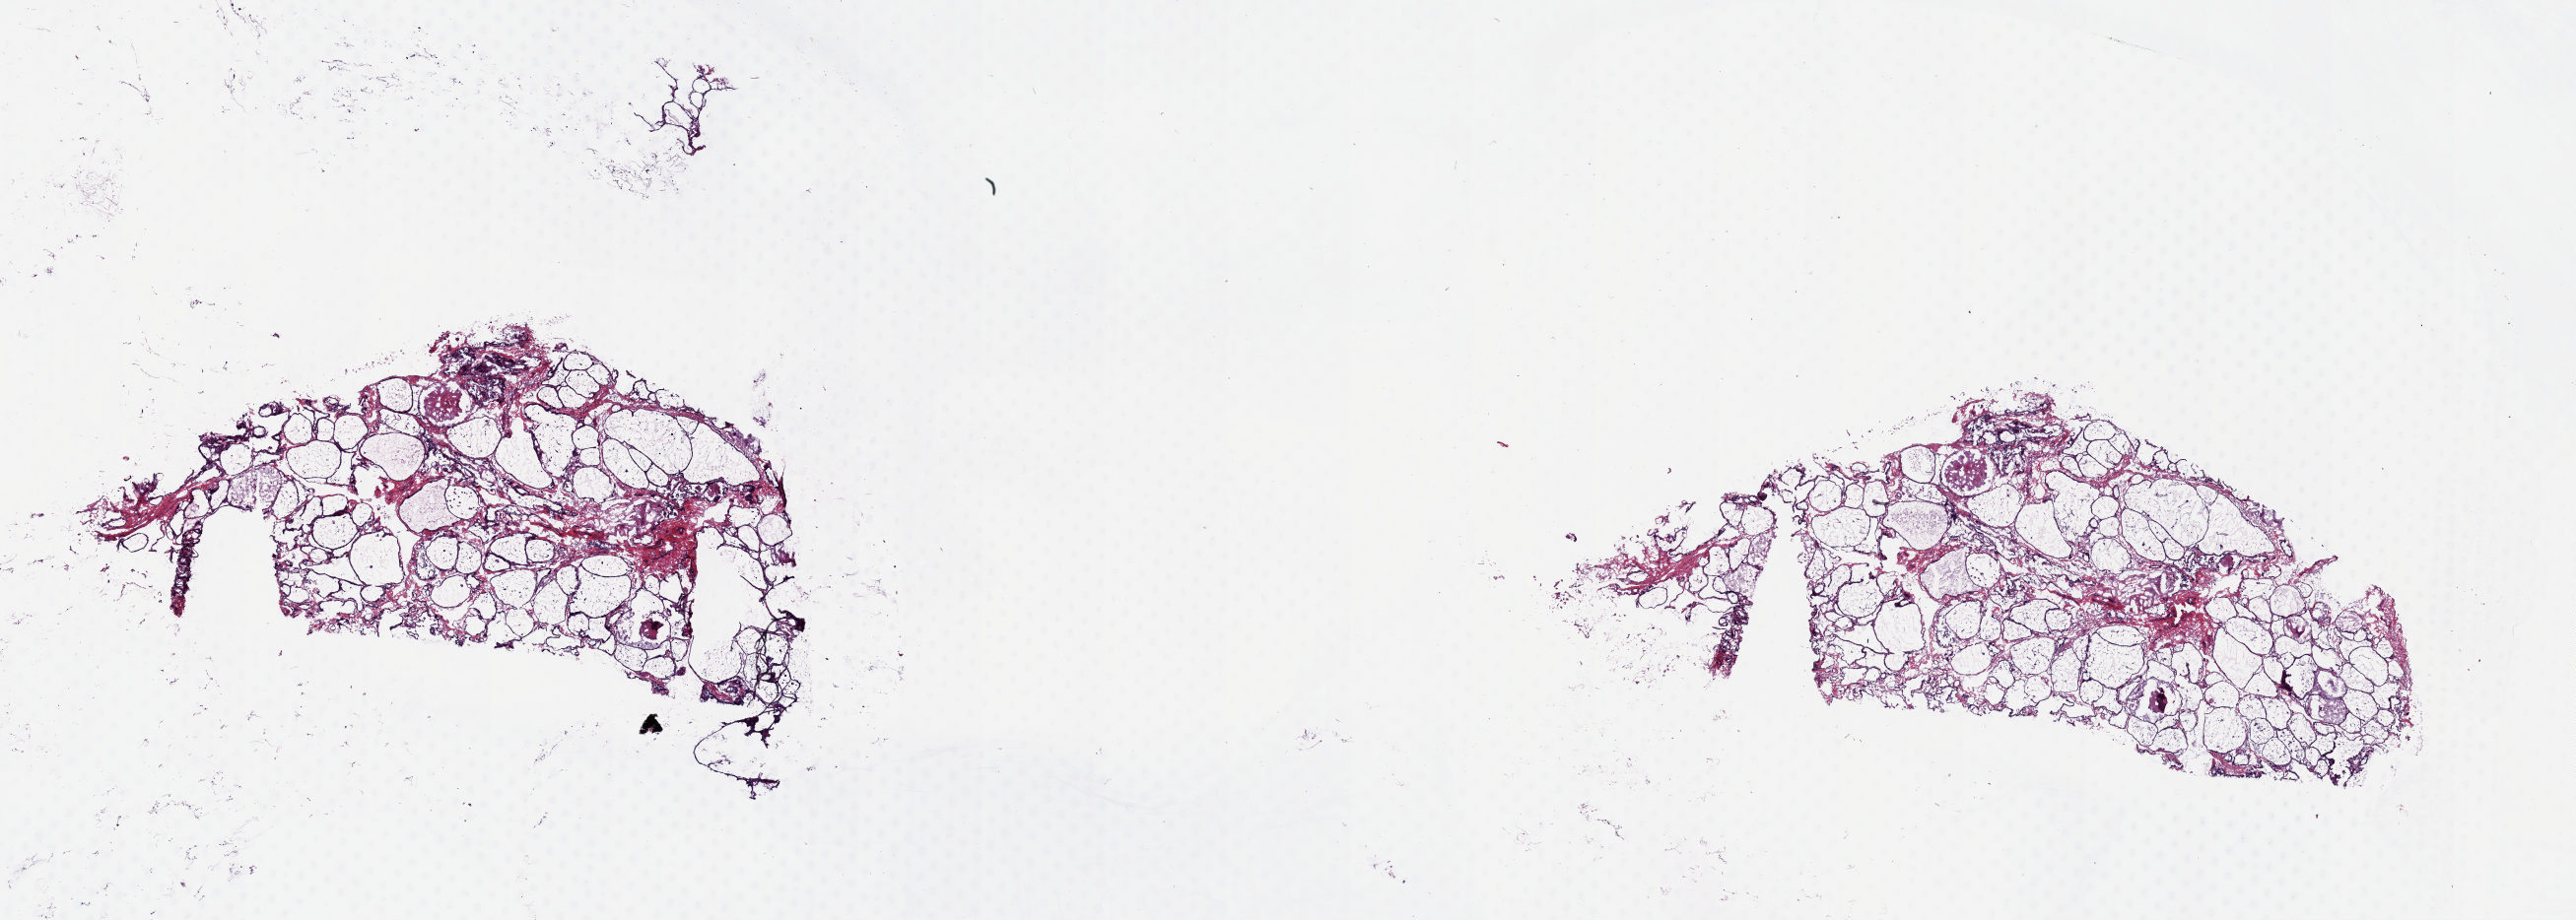
Whole-slide histology image, H&E-stained — shown as a low-resolution overview of the whole scanned area (about 20.6 x 7.4 mm, from a 20x scan); frozen section; solid tissue normal (non-tumour tissue) sample from the thyroid. Female, age 37 years at initial diagnosis. Slide review estimates, as recorded: tumour cells 0%, tumour nuclei 0%, normal cells 100%, stromal cells 0%, necrosis 0%. Inflammatory infiltration, as recorded: lymphocyte infiltration 0%, monocyte infiltration 0%, neutrophil infiltration 0%.
* this section: solid tissue normal (non-tumour) sample from the same patient
* patient diagnosis: Papillary adenocarcinoma, NOS